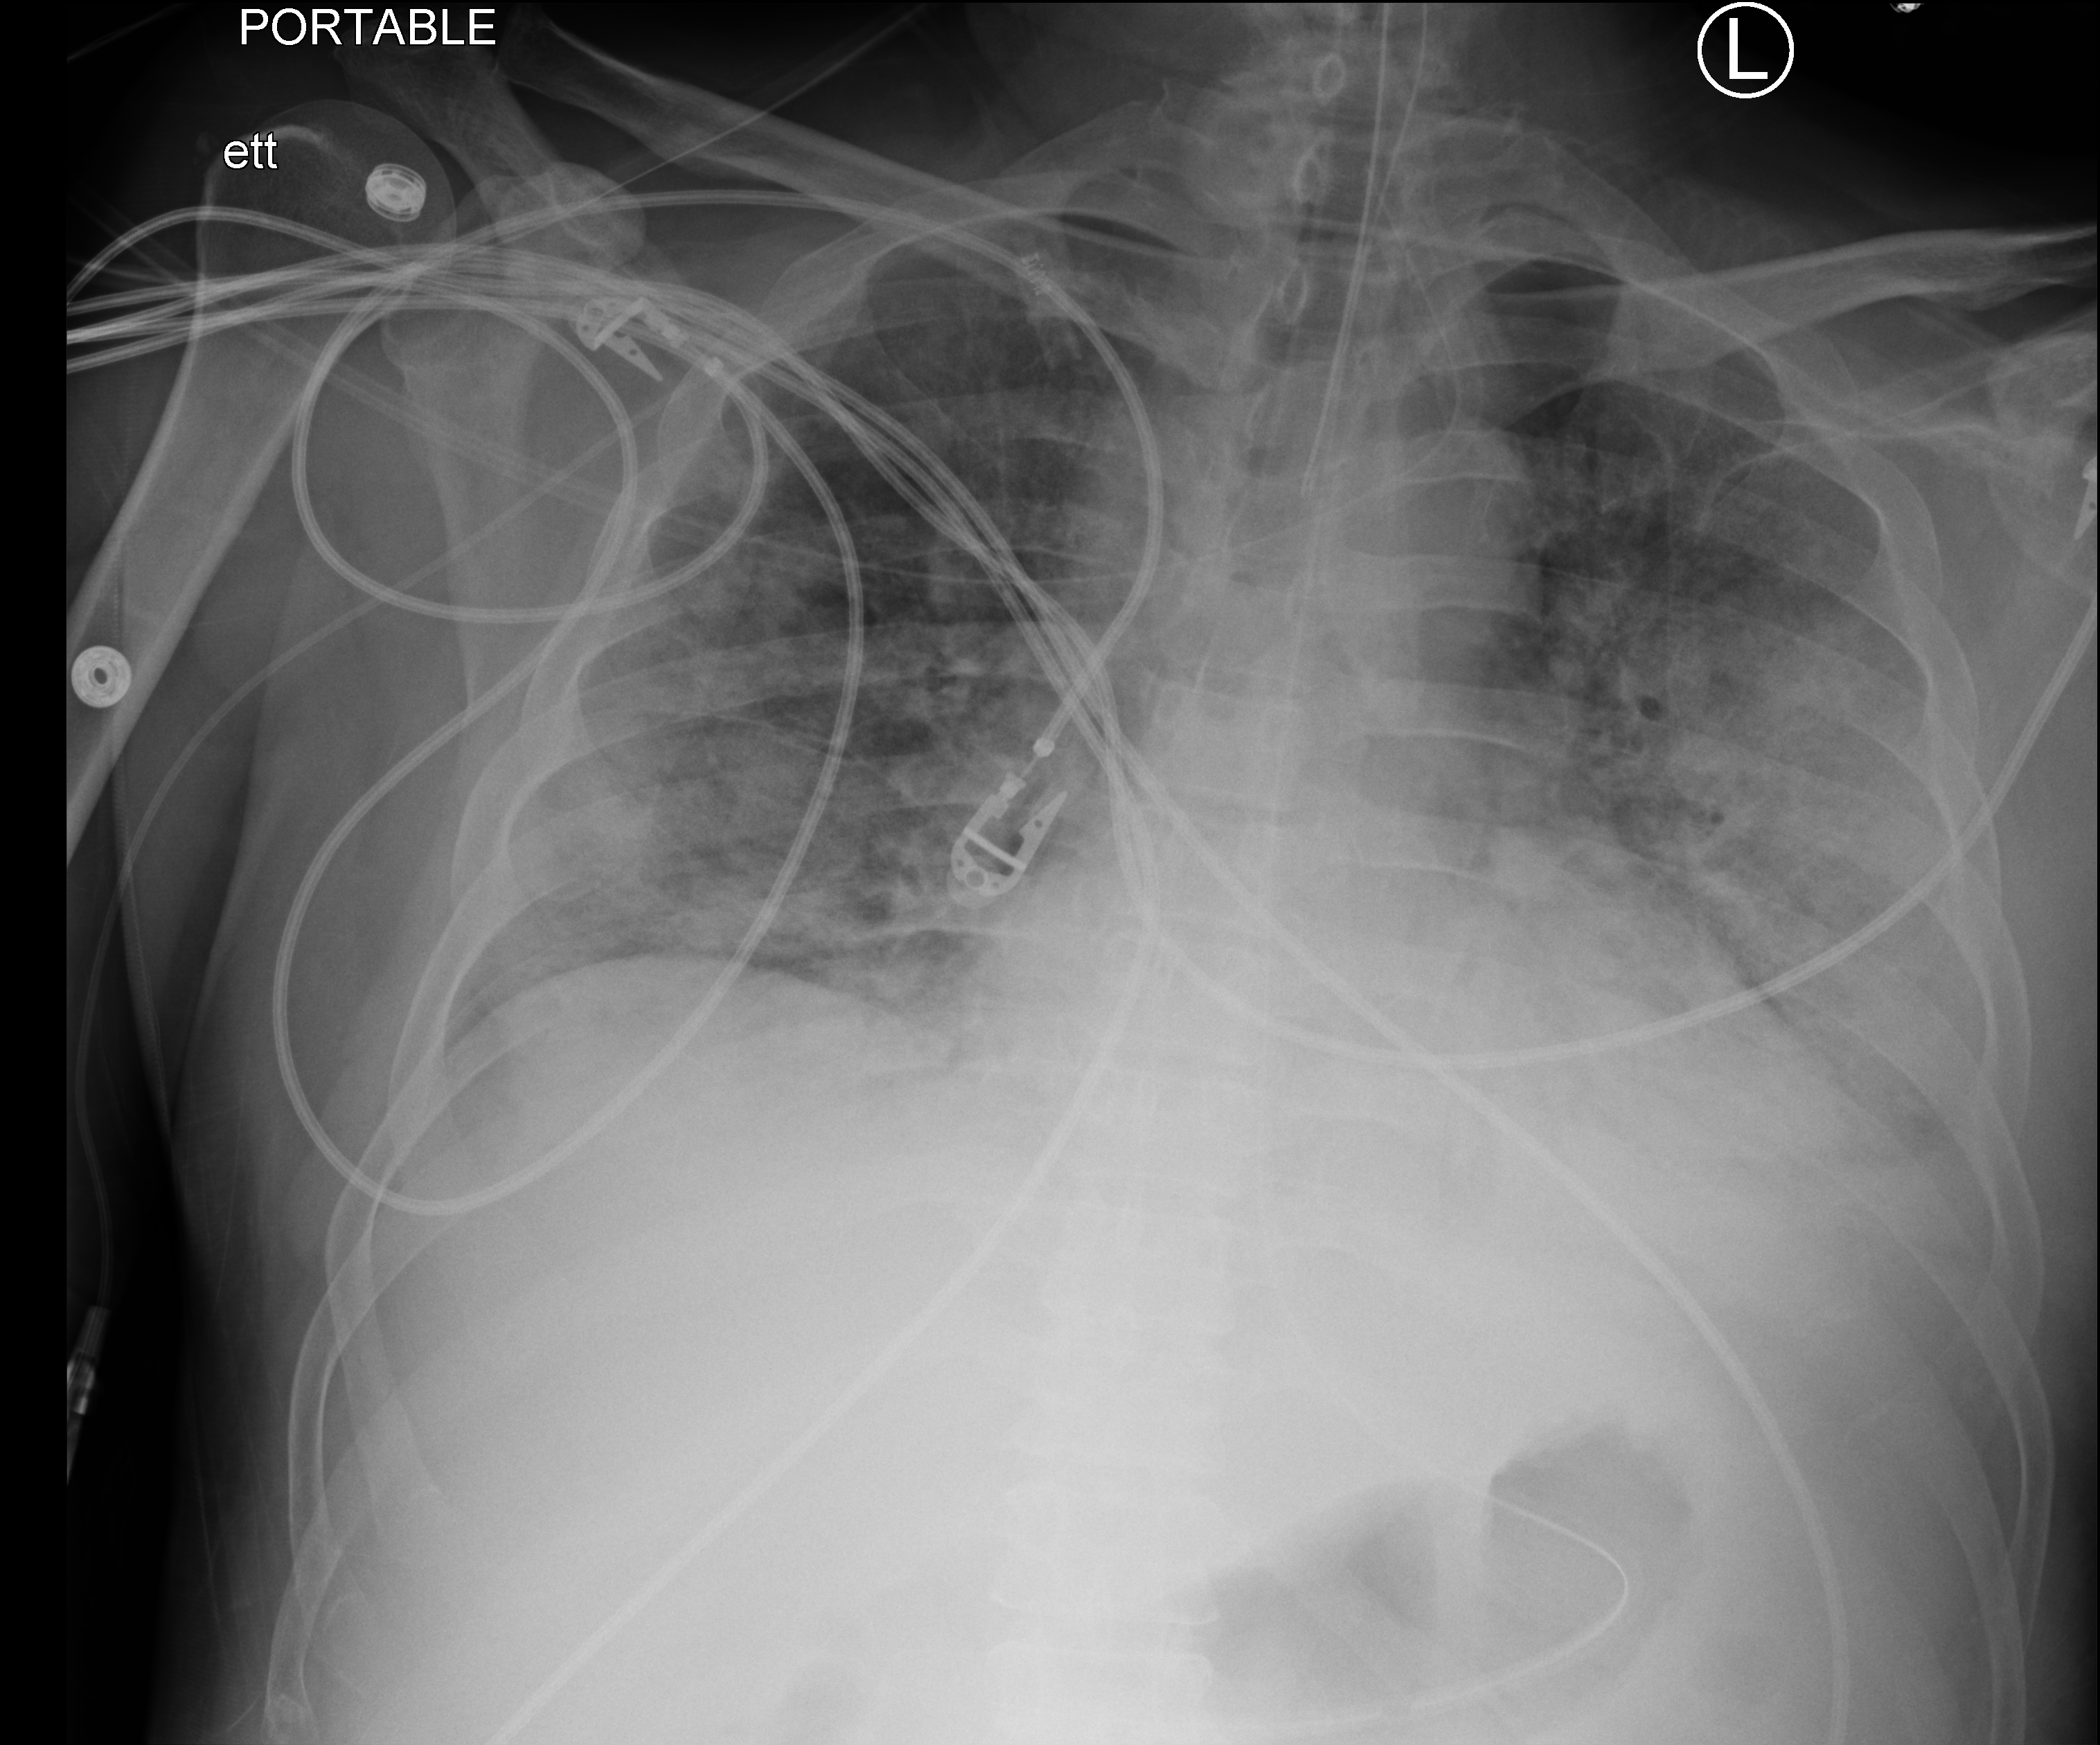
Bedside chest radiograph (computed radiography); anteroposterior (AP) projection. Male patient hospitalised with COVID-19, age 18–59 years.
Admission-level facts for this patient (not findings on this image; timing relative to this image not recorded): chronic kidney disease (admission record): no; admitted to intensive care during this hospital stay: yes.